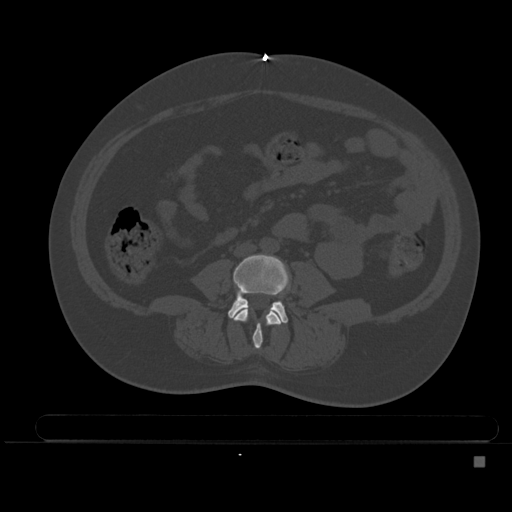
CT including the spine, one axial slice; position 138 of 495 along the scan axis; bone window (W 1800 / L 400 HU); 1.5 mm slice thickness; 512 × 512 image matrix, field of view 404 × 404 mm. Female patient, age 33 years. Case-level facts recorded for this patient, not image findings: primary cancer: breast; vertebrae with lytic lesions (as recorded): T1.
Annotated regions visible in this slice (semi-automatically segmented with operator editing):
- L3 vertebra: box from (x=234, y=308) to (x=282, y=349) px
- L4 vertebra: (x=228, y=254)–(x=289, y=323)